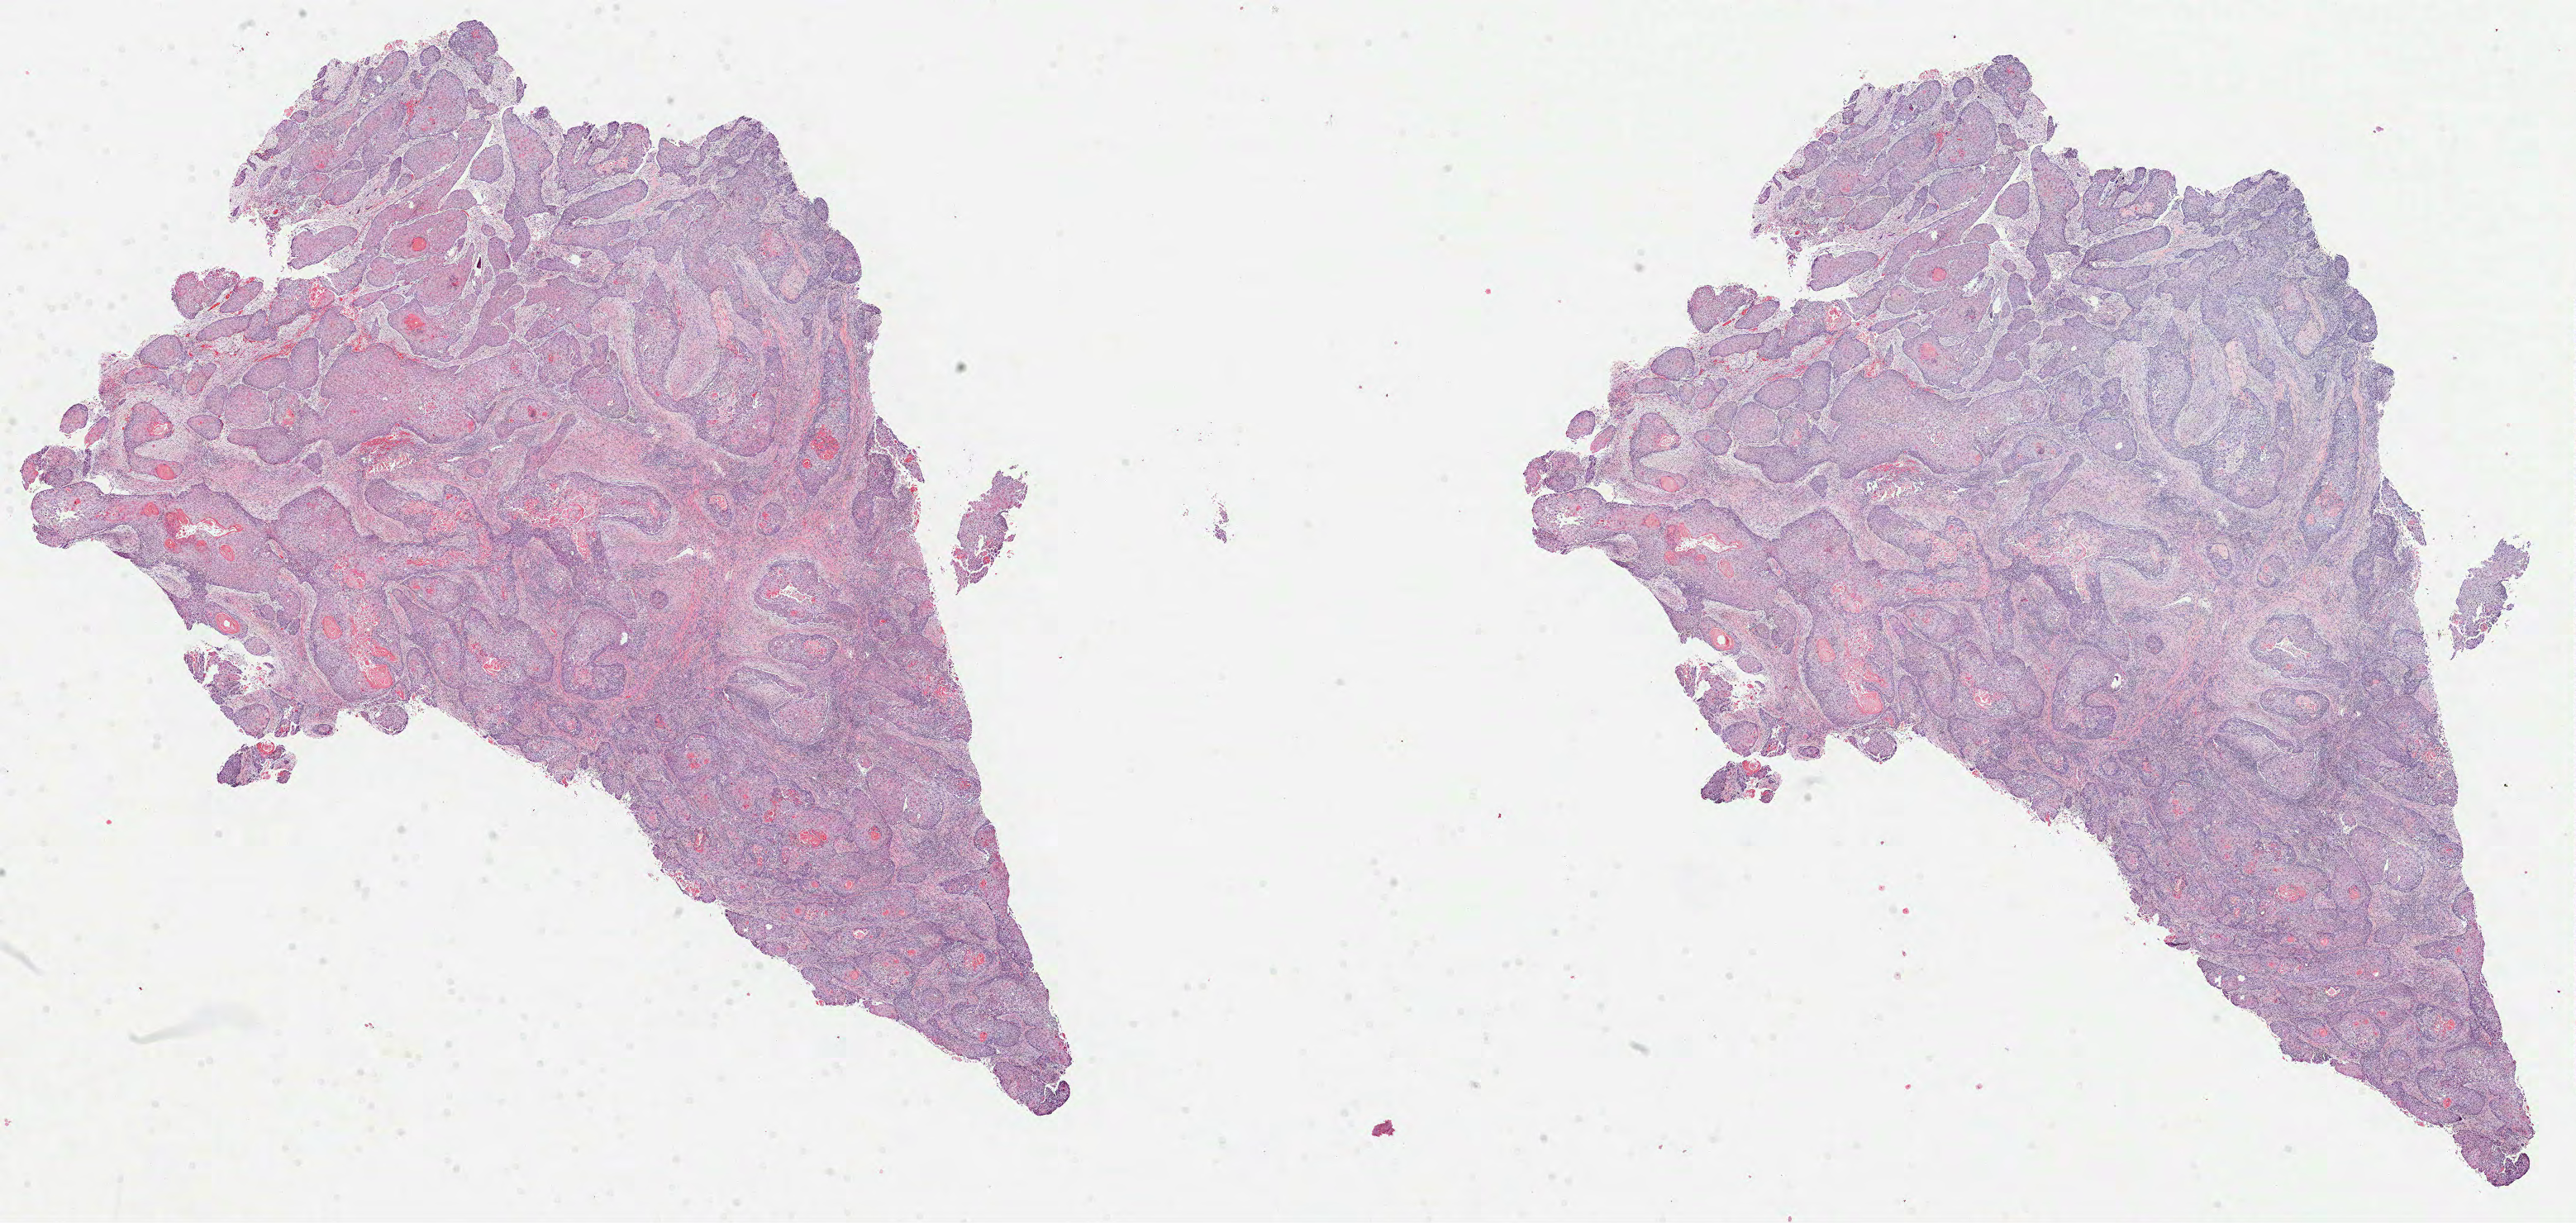
H&E whole-slide image, a low-resolution overview of the entire scanned area, about 25.1 x 11.9 mm; formalin-fixed paraffin-embedded (FFPE) diagnostic section; sample: primary tumour, head and neck. Male, age 67 years at initial diagnosis. Histologic grade: G2 (moderately differentiated).
AJCC pathologic stage: IVA (7th edition). Lymph nodes positive (case pathology): 0 of 37 examined. TNM: T4a N0. Diagnosis: Squamous cell carcinoma, NOS (overlapping lesion of lip, oral cavity and pharynx).